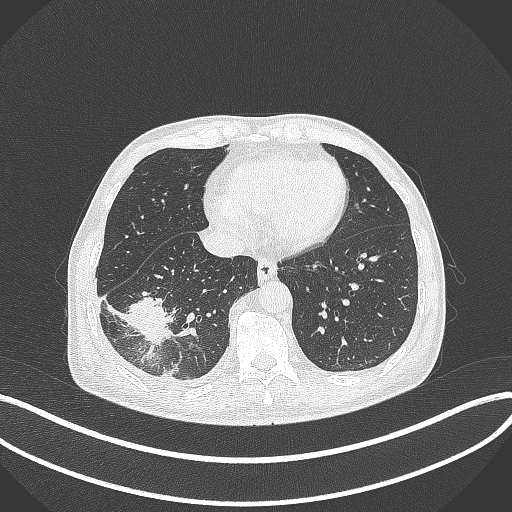
Chest CT, one axial slice; slice 111 of 388 in the series (ordered by position); reconstruction kernel B70f; 120 kVp; lung window (W 1500 / L -600 HU); 1 mm slice thickness; 512 × 512 image matrix. Male patient, age 64 years. From the clinical record (not read from this slice): clinical TNM (as recorded): T3 N0 M0; histopathological grade: G2-3.
Annotated regions visible in this slice (bounding box drawn by a radiologist):
- lung tumour (recorded histology: adenocarcinoma): bounding box <128,292,178,348> (left, top, right, bottom; pixels)